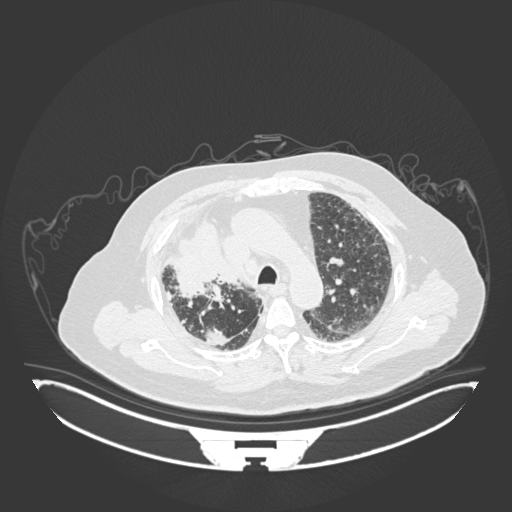
Chest CT, one axial slice; slice 131 of 201 in the series (ordered by position); 120 kVp; lung window (W 1500 / L -600 HU); 1 mm slice thickness; 512 × 512 image matrix, field of view 500 × 500 mm. Male patient, age 69 years. From the clinical record (not read from this slice): clinical TNM (as recorded): T4 N3 M1.
Structures marked on this image (bounding box drawn by a radiologist):
- lung tumour (recorded histology: adenocarcinoma): box from (x=170, y=216) to (x=247, y=306) px